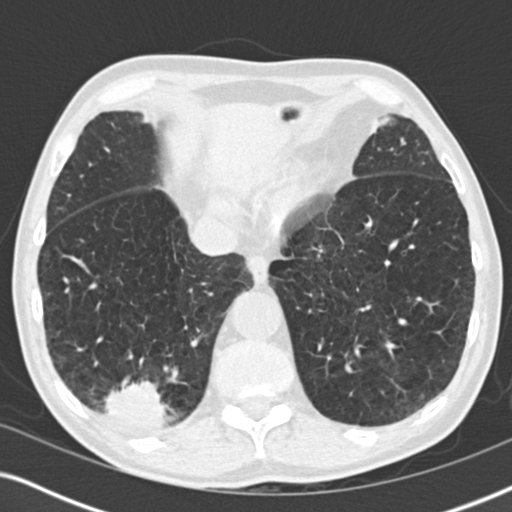
Low-dose screening chest CT, one axial slice; slice 57 of 196 in the series (ordered by position); reconstruction kernel B30f; 120 kVp; lung window (W 1500 / L -600 HU); 512 × 512 image matrix, field of view 330 × 330 mm.
Annotated regions visible in this slice (outlined manually by an expert reader):
- lesion 3 (tumor, lower lobe of right lung): bounding box [x1, y1, x2, y2] px = [104, 381, 166, 429]